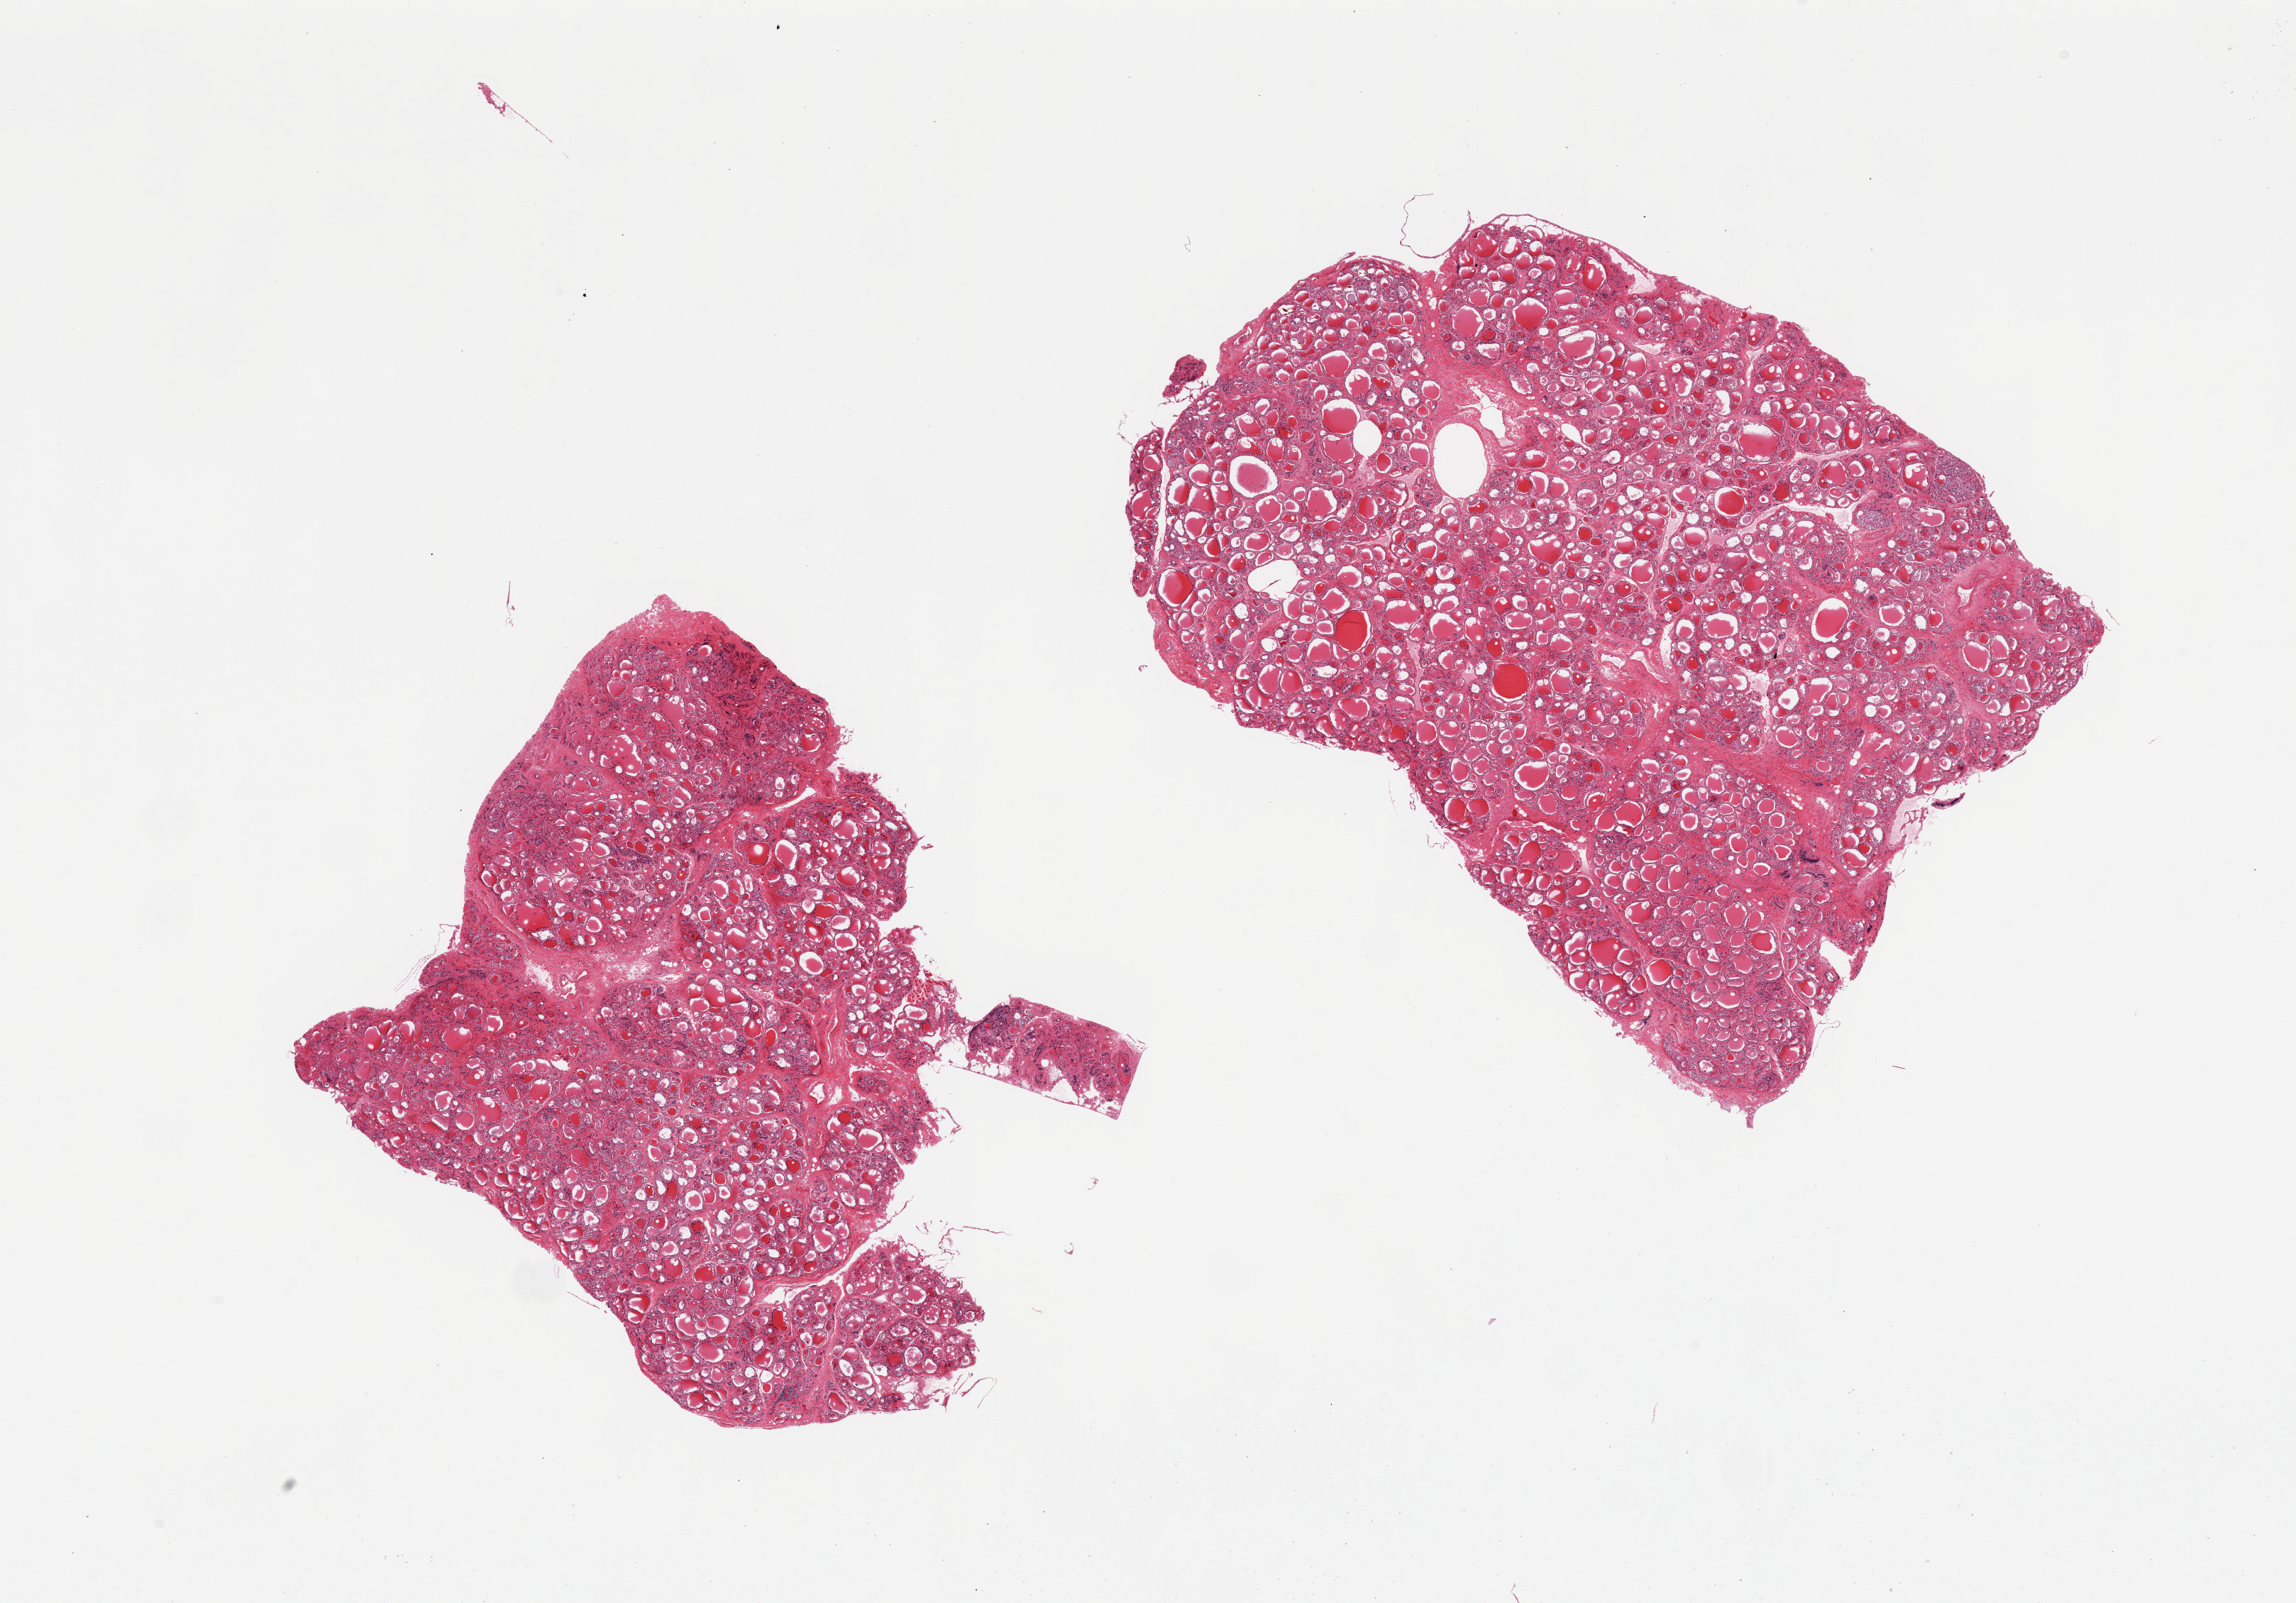
H&E whole-slide image — shown as a low-resolution overview of the whole scanned area (about 25.6 x 17.9 mm), PAXgene-fixed paraffin-embedded (PFPE) section, sampled site (target tissue): thyroid, tissue donor sample.
Review note (as recorded): 2 pieces, features of goitre, regressive changes.